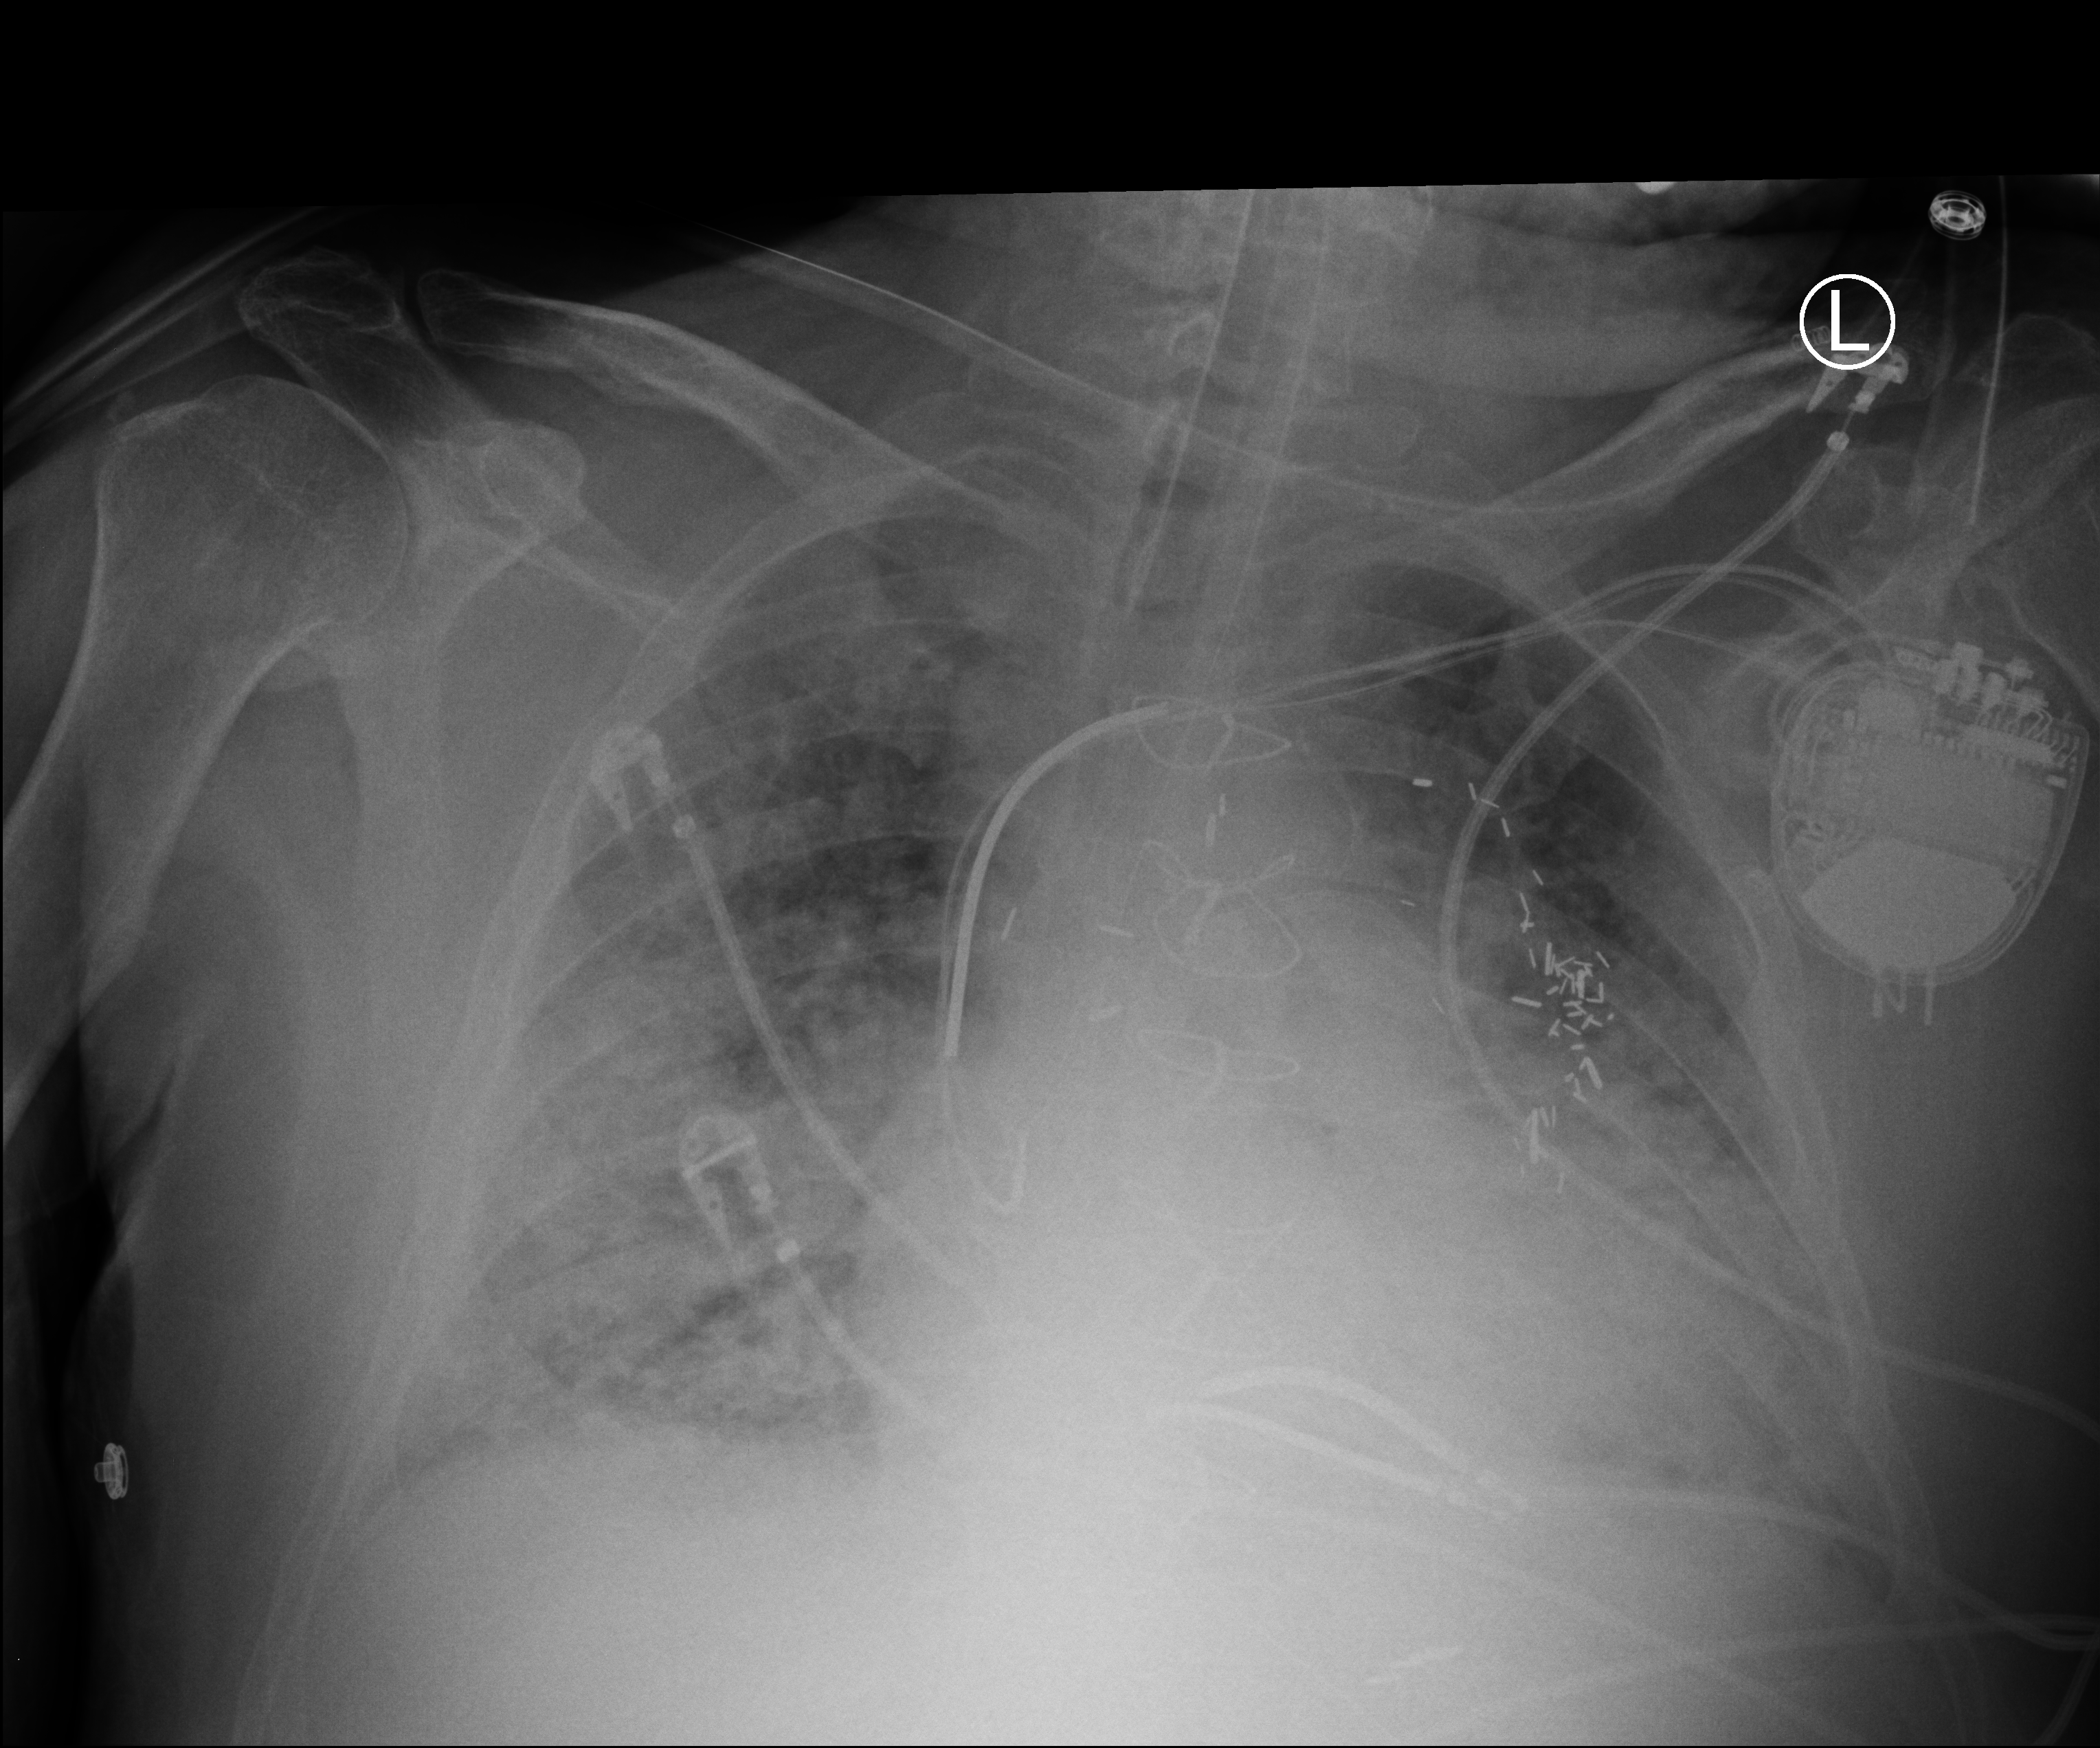
Chest X-ray (portable), anteroposterior (AP) projection. Patient hospitalised with COVID-19; male, aged 60–74 years.
Hospital-stay facts (about this admission, not read from this image; timing relative to this image not recorded):
- chronic kidney disease (admission record): no
- mechanically ventilated during this hospital stay: yes
- smoking status (admission record): never